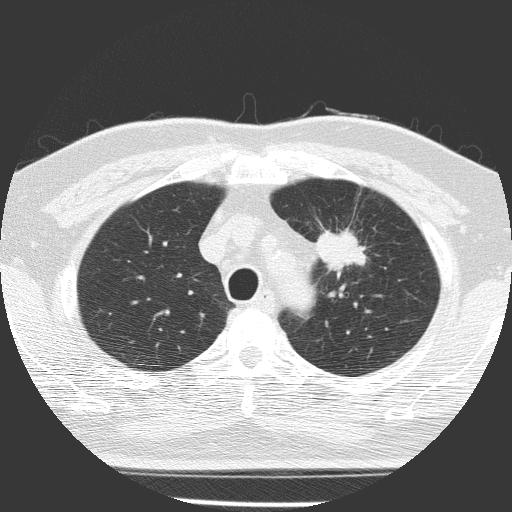
Low-dose screening chest CT, one axial slice. Position 119 of 156 along the scan axis. Reconstruction kernel FC51. 120 kVp. Lung window (W 1500 / L -600 HU). 2 mm slice thickness. 512 × 512 image matrix, field of view 309 × 309 mm.
Annotated regions visible in this slice (expert manual segmentation):
- lesion 1 (tumor, upper lobe of left lung): bounding box (x1, y1, x2, y2) in pixels: (316, 230, 367, 273)